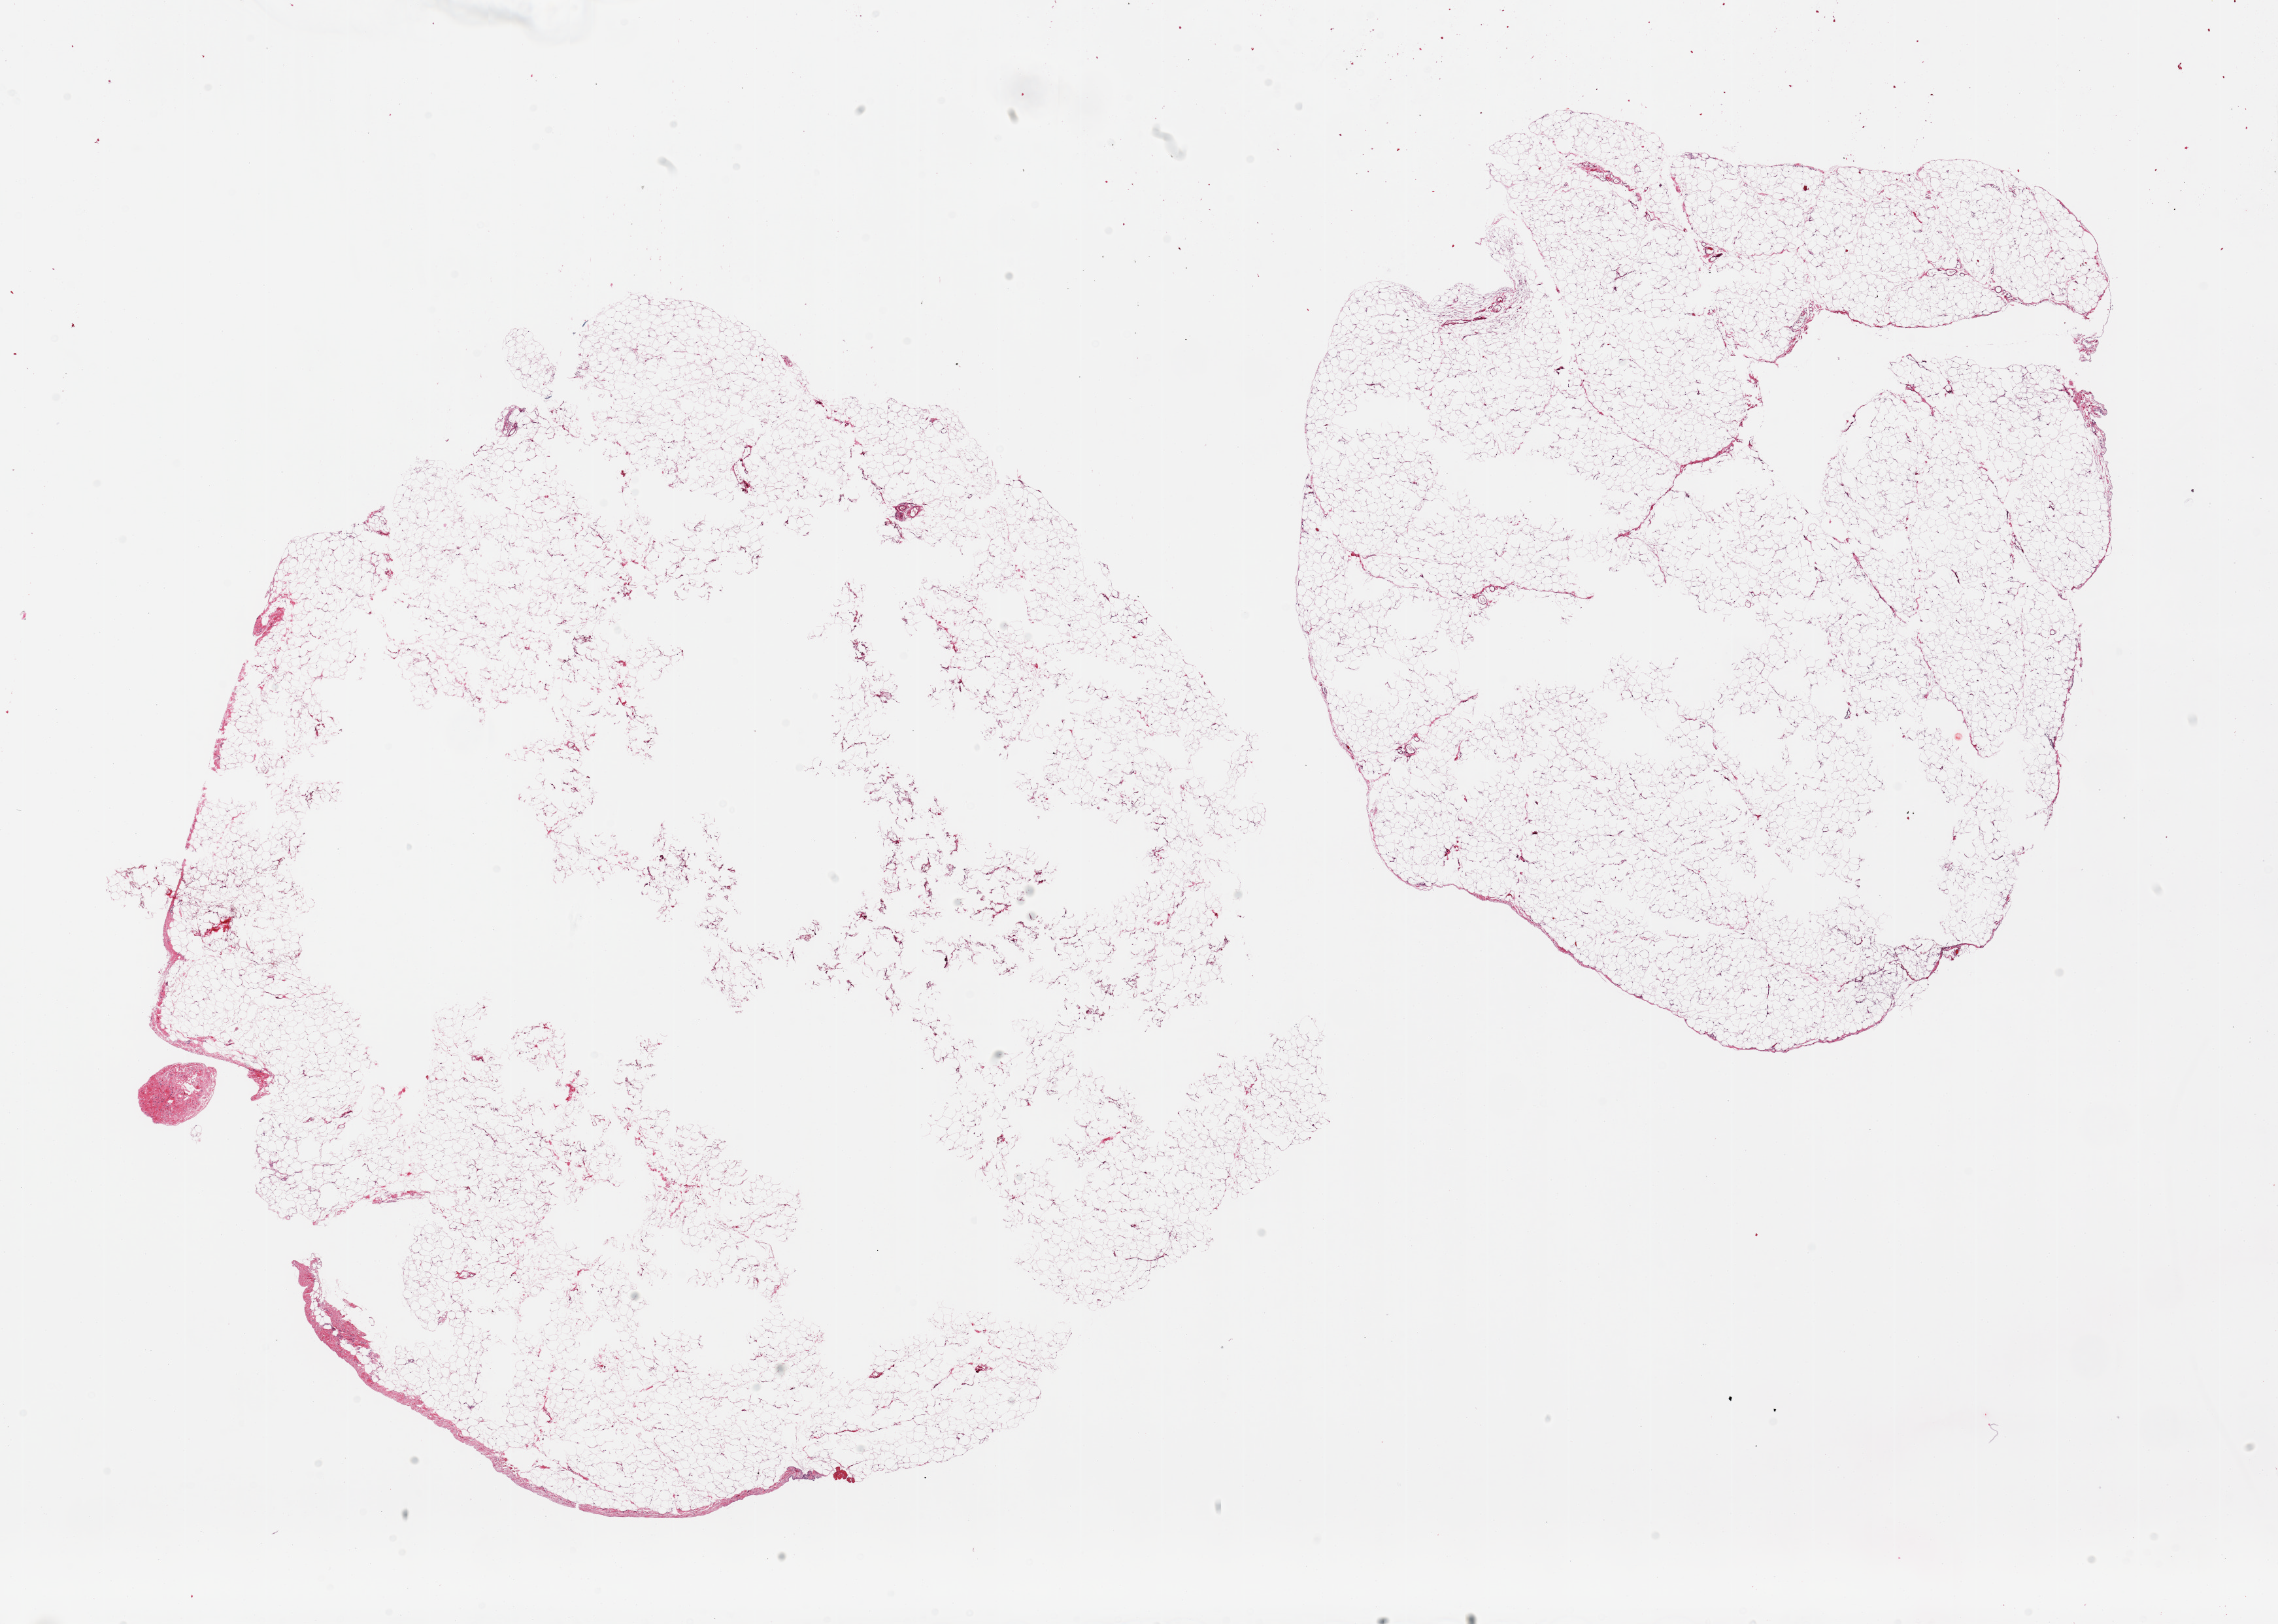
Whole-slide image, hematoxylin and eosin (H&E) stain, brightfield, a low-resolution overview of the entire scanned area, about 27.6 x 19.7 mm; PAXgene-fixed, paraffin-embedded tissue; target tissue: omentum; tissue donor sample.
• review note (as recorded): 2 pieces; mature adipose tissue, central defects (?poor fixation)